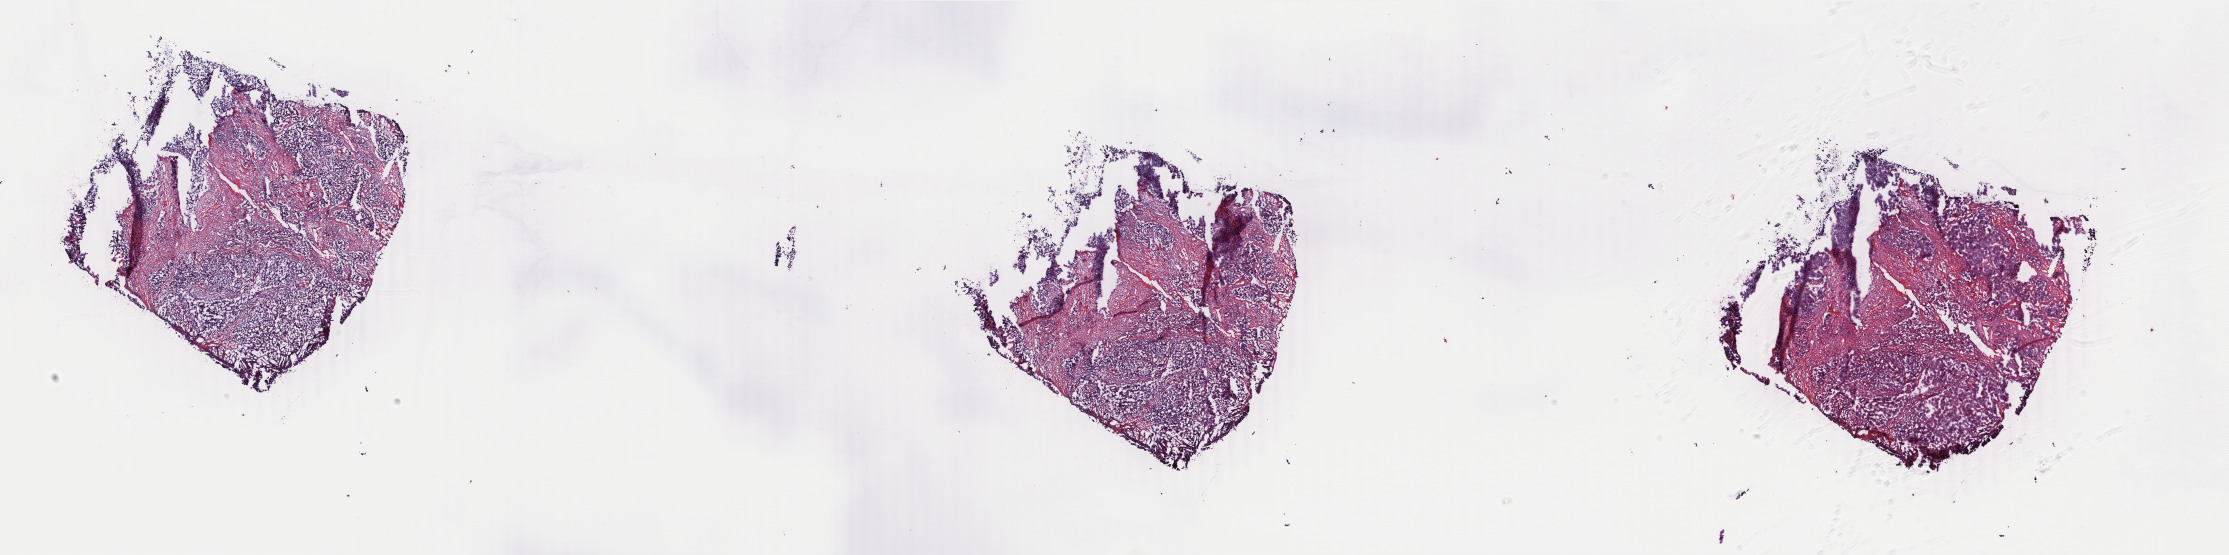
Digitized Hematoxylin and eosin (H&E) stained tissue section (whole slide) — shown as a low-resolution overview of the whole scanned area (about 35.5 x 8.8 mm, acquisition: 40x scan); frozen section from the bottom of the tissue portion; breast, primary tumour sample. Female patient; age at initial diagnosis 40 years. Composition of this section per pathologist review: tumour cells 85%, tumour nuclei 85%, normal cells 0%, stromal cells 15%, necrosis 0%. Infiltration values recorded for this section: lymphocyte infiltration 1%, monocyte infiltration 0%, neutrophil infiltration 0%.
• histologic diagnosis: Infiltrating duct carcinoma, NOS
• AJCC pathologic stage: IIIA (4th edition)
• lymph nodes positive (case pathology): 1 of 26 examined